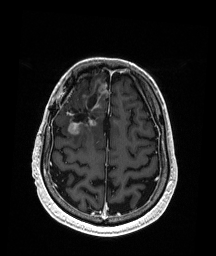
Brain MRI from a brain-tumour surgery series, one axial slice; slice 53 of 192 in the series (ordered by position); T1-weighted post-contrast; 1 mm slice thickness; 216 × 256 image matrix, field of view 211 × 250 mm. Case-level facts recorded for this patient, not image findings: histopathology: Astrocytoma; WHO grade: 3; IDH mutation: yes; tumour location: Right Frontal.
Structures marked on this image (outlined manually by an expert reader):
- previous resection cavity: bounding box <65,93,98,124> (left, top, right, bottom; pixels)
- tumour: <68,85,108,136>